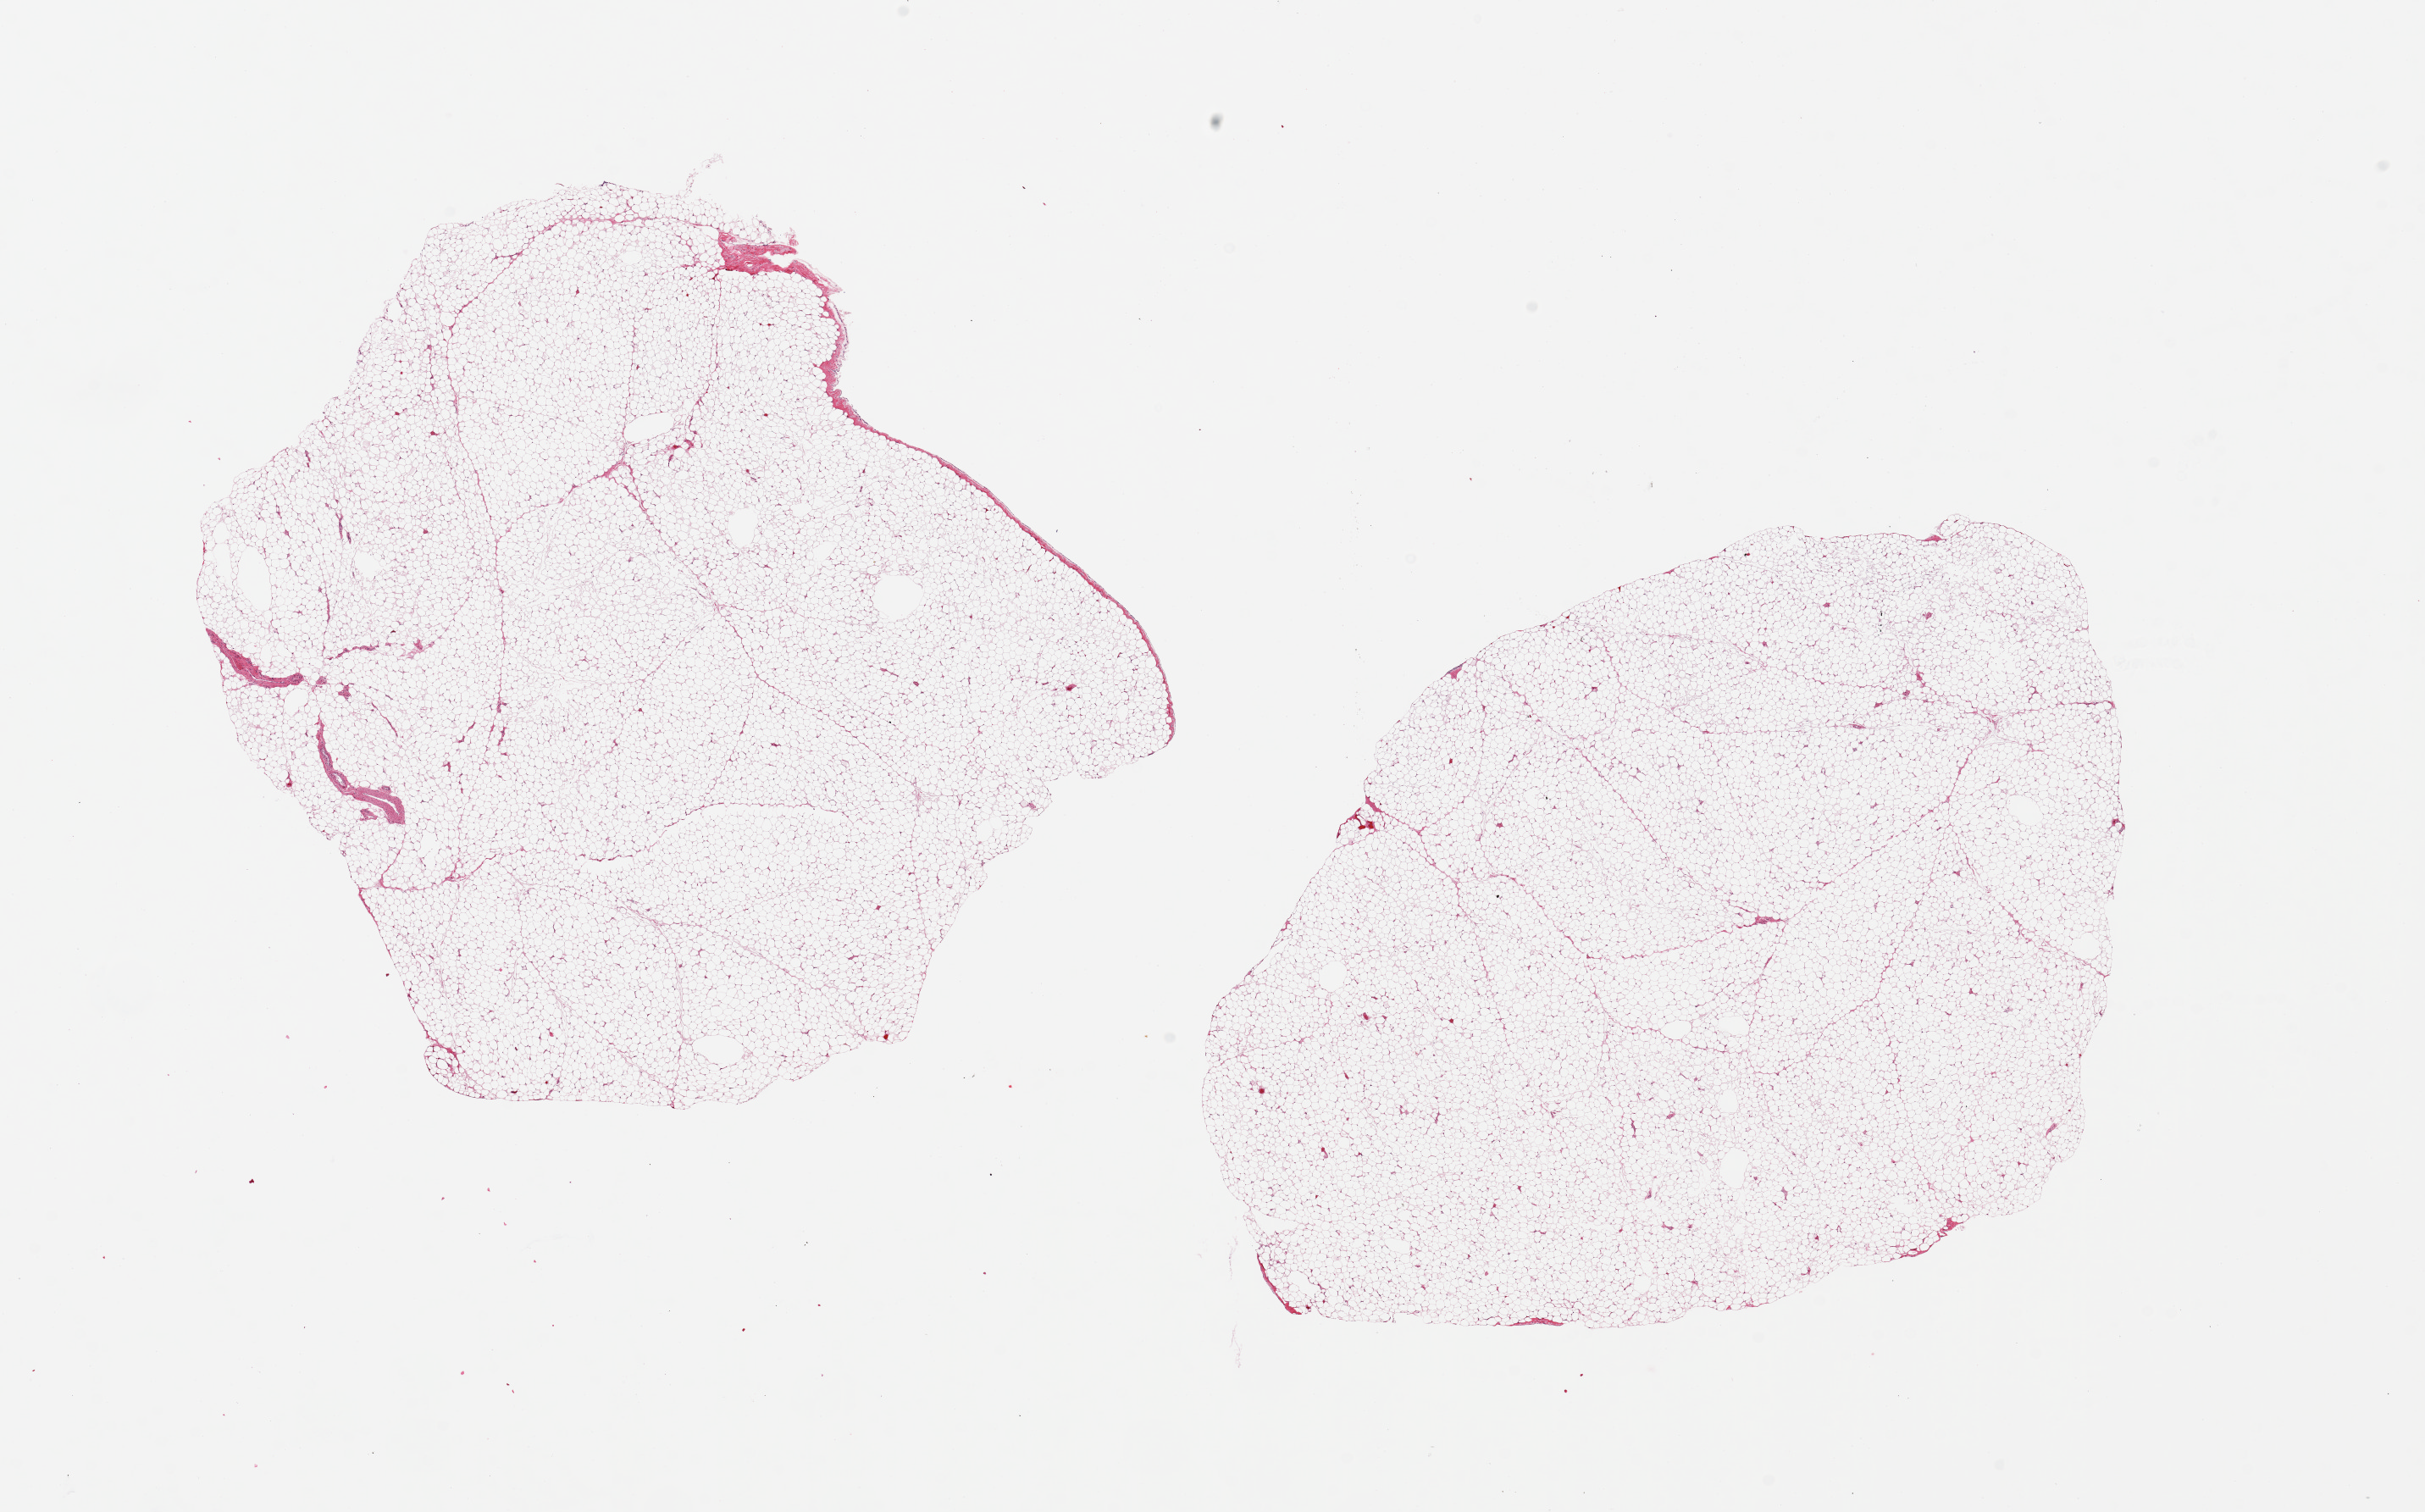
Digitized H&E-stained section — whole scanned area (about 22.6 x 14.1 mm, acquisition: 20x scan) shown as a low-resolution overview, PAXgene-fixed, paraffin-embedded tissue, section of omentum (target tissue), tissue donor sample. Donor: male.
Review note (as recorded): 2 pieces ~7x7mm.